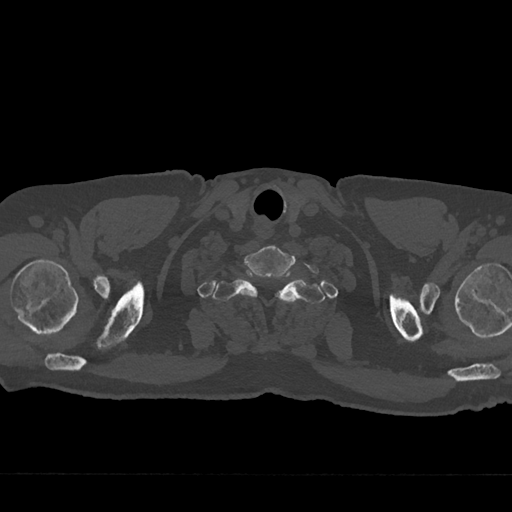
CT including the spine, one axial slice. Position 674 of 797 along the scan axis. Reconstruction kernel Br40s/3. 120 kVp. Bone window (W 1800 / L 400 HU). 0.5 mm slice thickness. 512 × 512 image matrix. Patient: male, 75 years. Case-level facts recorded for this patient, not image findings: primary cancer: renal.
Annotated regions visible in this slice (semi-automatic segmentation, software-assisted and operator-edited):
- T1 vertebra: bounding box [x1, y1, x2, y2] px = [213, 271, 325, 304]
- T2 vertebra: [278, 292, 280, 294]